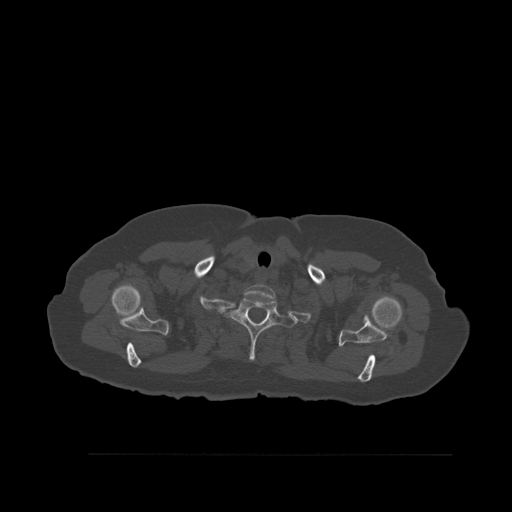
CT including the spine, one axial slice; position 444 of 527 along the scan axis; bone window (W 1800 / L 400 HU); 1.5 mm slice thickness; 512 × 512 image matrix, field of view 470 × 470 mm. Patient: female, 73 years. Case-level facts recorded for this patient, not image findings: primary cancer: breast.
Structures marked on this image (semi-automatic segmentation, software-assisted and operator-edited):
- T1 vertebra: bounding box (x1, y1, x2, y2) in pixels: (220, 297, 297, 361)